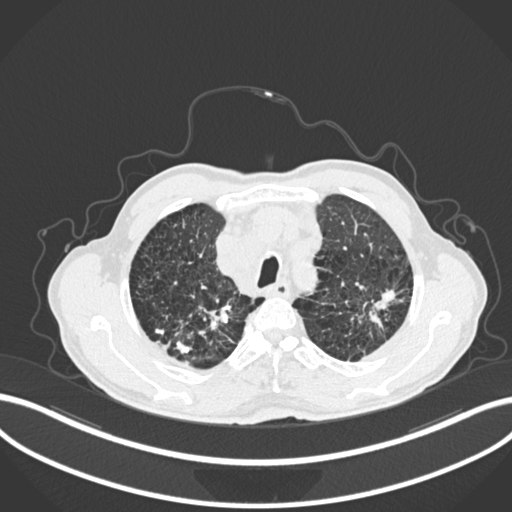
Chest CT, one axial slice. Position 226 of 287 along the scan axis. Reconstruction kernel B30f. 120 kVp. Lung window (W 1500 / L -600 HU). 512 × 512 image matrix, field of view 400 × 400 mm. Patient: male, 74 years. Case-level facts recorded for this patient, not image findings: clinical TNM (as recorded): T2a N1 M0.
Outlined on this slice (bounding box drawn by a radiologist):
- lung tumour (recorded histology: adenocarcinoma): bounding box [x1, y1, x2, y2] px = [369, 286, 401, 332]